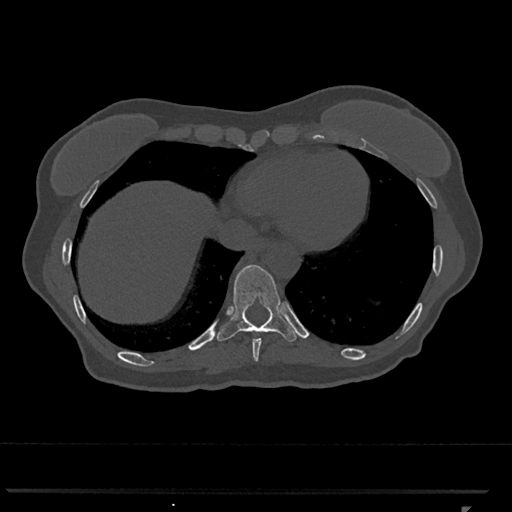
CT including the spine, one axial slice. Slice 581 of 793 in the series (ordered by position). Reconstruction kernel Br40s/3. Bone window (W 1800 / L 400 HU). 512 × 512 image matrix. Female patient, age 62 years. Case-level facts recorded for this patient, not image findings: primary cancer: renal.
Outlined on this slice (semi-automatically segmented with operator editing):
- T10 vertebra: bounding box <217,264,298,342> (left, top, right, bottom; pixels)
- T9 vertebra: <252,333,282,362>